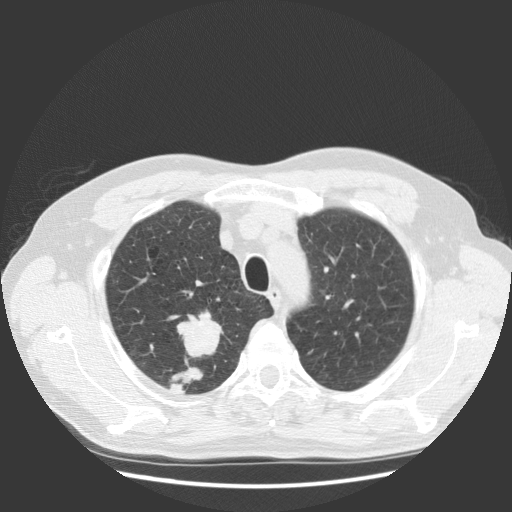
Low-dose screening chest CT, one axial slice. Slice 102 of 131 in the series (ordered by position). Reconstruction kernel STANDARD. 140 kVp. Lung window (W 1500 / L -600 HU). 512 × 512 image matrix, field of view 369 × 369 mm.
Outlined on this slice (outlined manually by an expert reader):
- lesion 1 (tumor, upper lobe of right lung): bounding box [x1, y1, x2, y2] px = [177, 310, 224, 358]
- lesion 2 (tumor, upper lobe of right lung): [169, 365, 203, 394]